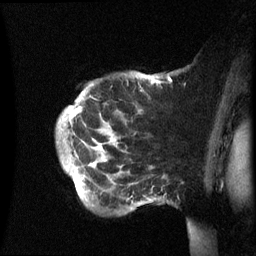
Breast MRI (dynamic contrast-enhanced), one sagittal slice. Position 49 of 60 along the scan axis. Dynamic contrast-enhanced series, image 2 of 3 at this slice position (ordered by acquisition). 1.5 T. TE 4.2 ms, TR 8.4 ms. 256 × 256 image matrix, field of view 230 × 230 mm. Patient: female, 49 years.
Annotated regions visible in this slice (semi-automatically segmented with operator editing):
- analysis volume of interest (the breast-tissue region the enhancement analysis was run in; not a lesion): bounding box <56,72,169,214> (left, top, right, bottom; pixels)
- tumour enhancement mask (voxels above the 70 % enhancement threshold inside the analysis volume of interest): <70,80,160,186>